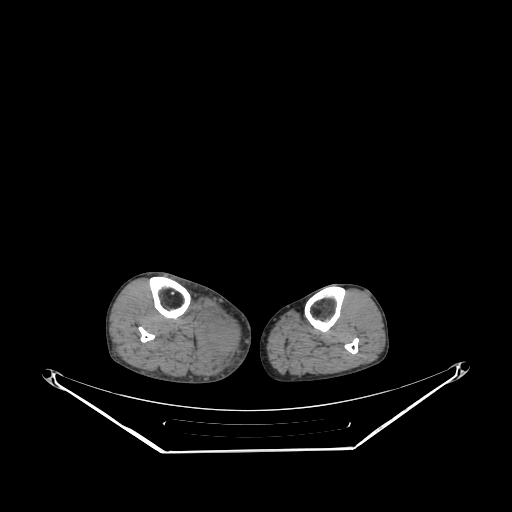
CT of an extremity soft-tissue mass (from a PET/CT study), one axial slice; slice 144 of 267 in the series (ordered by position); reconstruction kernel SOFT; 140 kVp; soft-tissue window (W 400 / L 40 HU); 3.75 mm slice thickness; 512 × 512 image matrix, field of view 500 × 500 mm. Male patient. Case-level facts recorded for this patient, not image findings: histological type: pleiomorphic liposarcoma; grade: high; site of the primary tumour: right calf.
Structures marked on this image (expert contour drawn on MRI and transferred to this co-registered scan by the dataset authors):
- gross tumour volume including surrounding oedema: bounding box <199,311,238,359> (left, top, right, bottom; pixels)
- gross tumour volume (mass): <210,320,234,352>